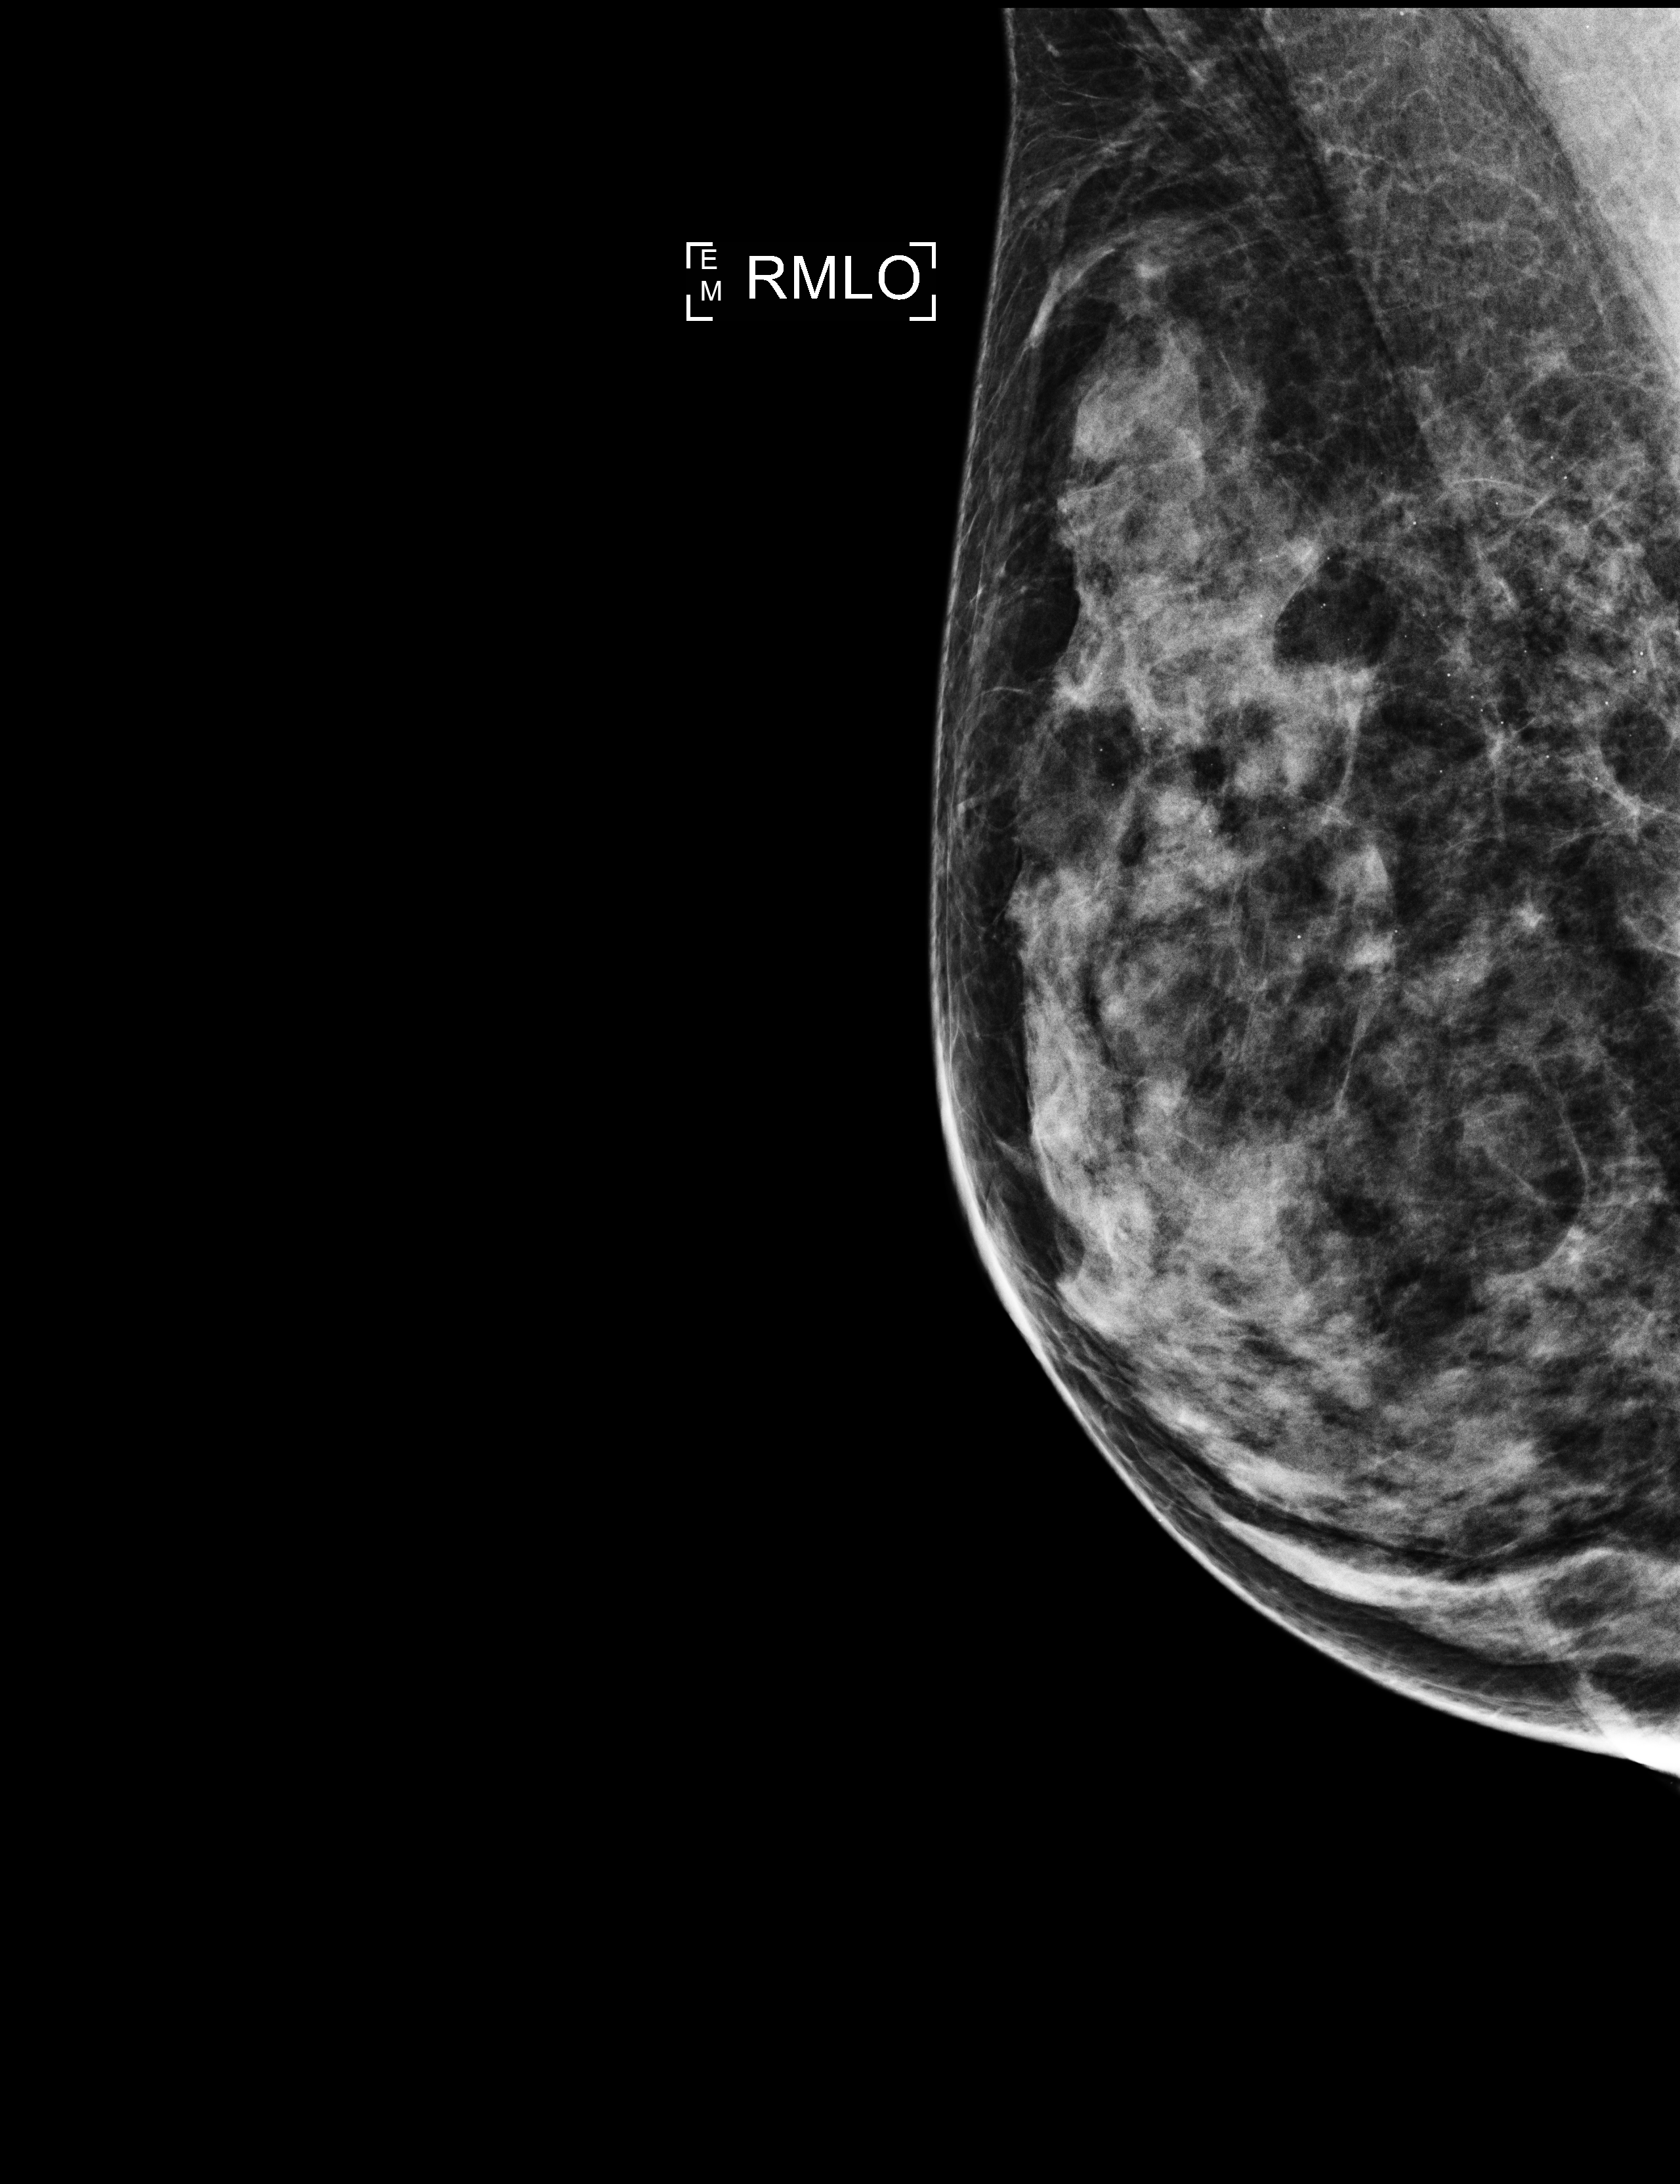
Digital mammogram (FFDM); right breast; mediolateral oblique (MLO) view; annual screening mammography examination; compressed breast thickness 44 mm. Patient: female, 46 years.
Breast density at the screening exam (both breasts): extremely dense (BI-RADS density category d). Final BI-RADS assessment for this screening round (tomosynthesis exam, both breasts): category 1. Recall: no recall after this screen.